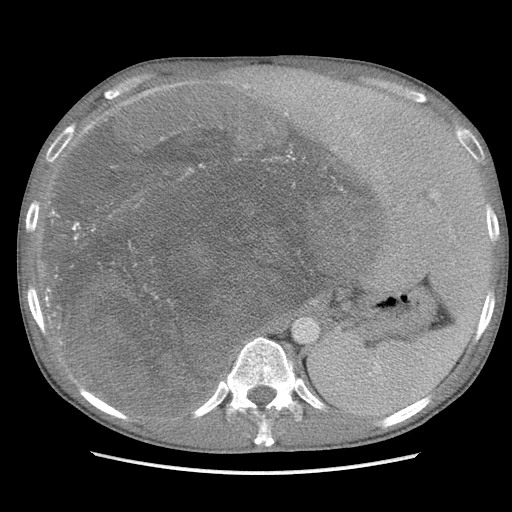
Contrast-enhanced abdominal CT, one axial slice; soft-tissue window (W 400 / L 40 HU); 5 mm slice thickness; 512 × 512 image matrix. Male patient. Case-level facts recorded for this patient, not image findings: diagnosis: adrenocortical carcinoma; tumour side: right adrenal; Ki-67 index: 13 %; stage (as recorded): 3.
Structures marked on this image (semi-automatically segmented with operator editing):
- mass: bounding box <50,86,374,410> (left, top, right, bottom; pixels)